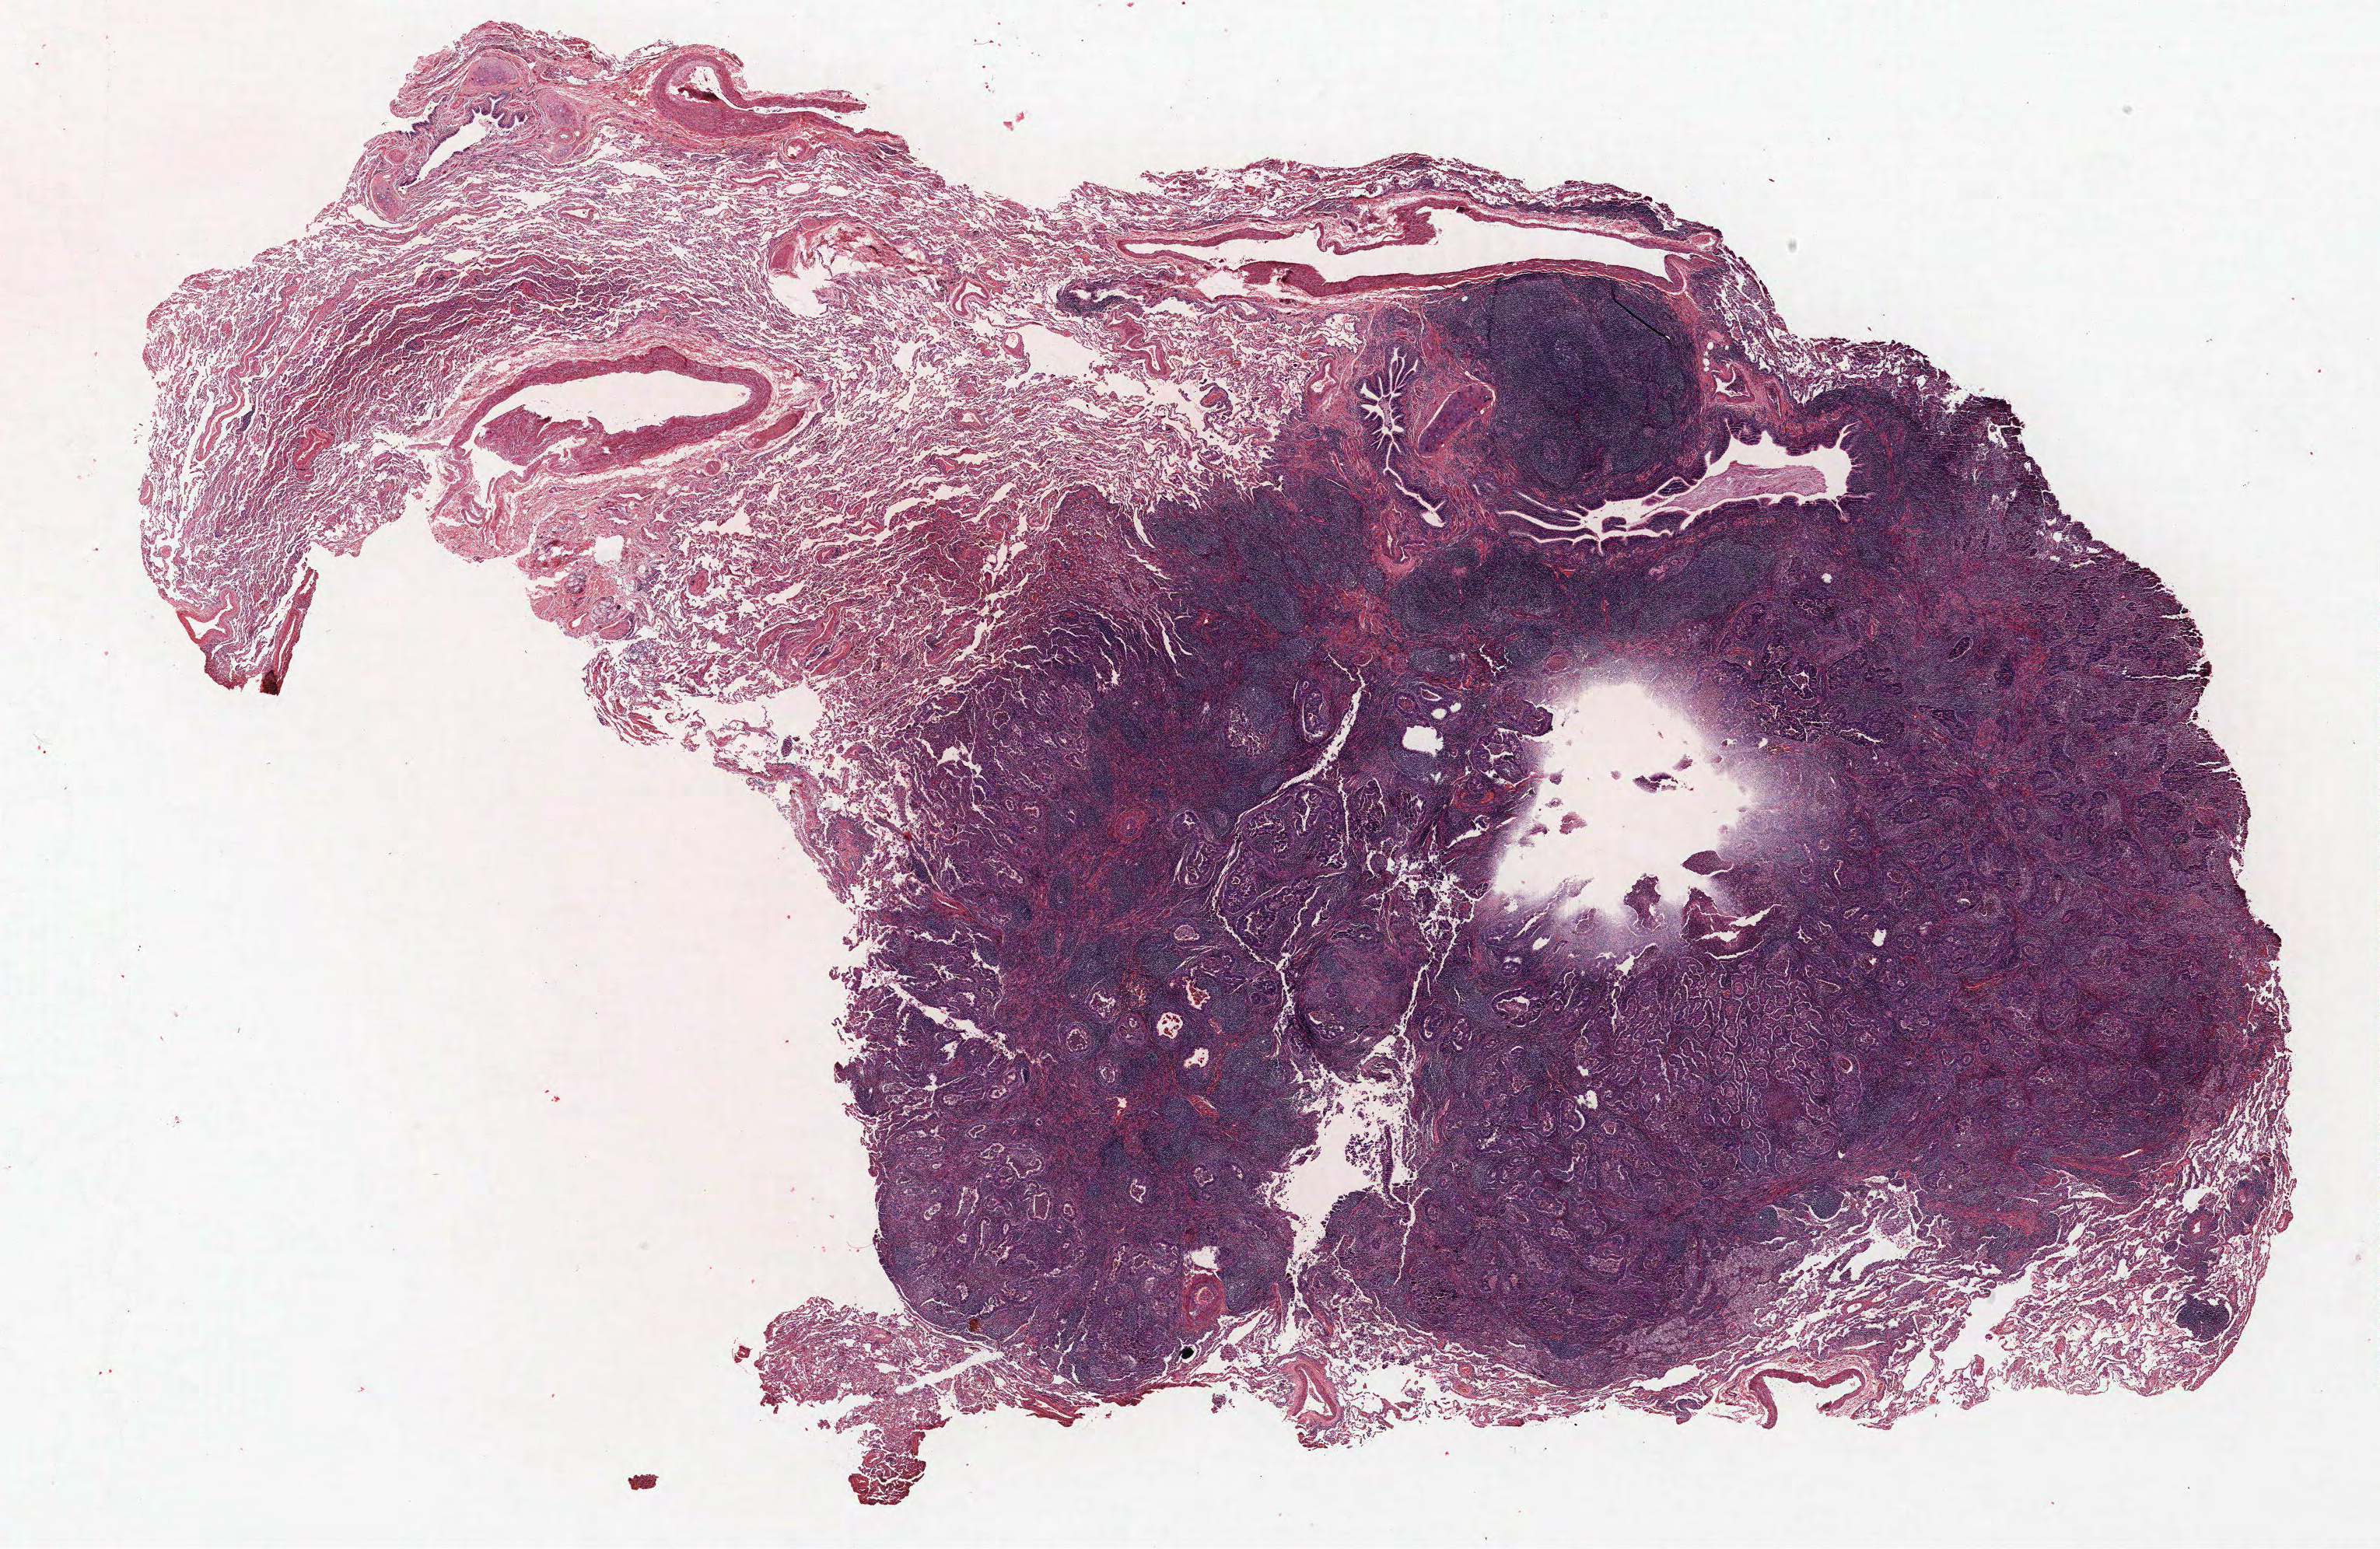
Hematoxylin and eosin (H&E) stained whole-slide image — low-resolution overview of the scanned area, about 24.5 x 15.9 mm, FFPE section, lung. Male patient, aged 55 at enrolment. Former smoker at enrolment. Grade: moderately differentiated (G2).
Stage (AJCC 6th edition): IA. Participant's lung-cancer diagnosis: Acinar cell carcinoma. Tumour size (pathology): 15 mm. Primary tumour location (clinical record): right upper lobe. Note: participant had 2 primary lung cancers recorded; fields above describe the first.